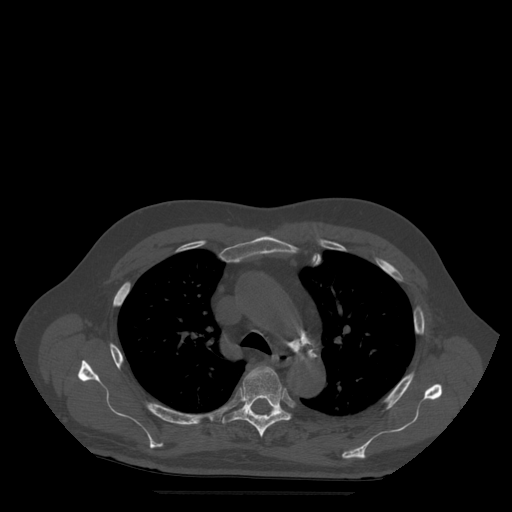
CT including the spine, one axial slice. Position 374 of 522 along the scan axis. Bone window (W 1800 / L 400 HU). 1.25 mm slice thickness. 512 × 512 image matrix, field of view 420 × 420 mm. Patient age 72 years. Case-level facts recorded for this patient, not image findings: primary cancer: prostate.
Structures marked on this image (semi-automatic segmentation, software-assisted and operator-edited):
- T5 vertebra: bounding box (x1, y1, x2, y2) in pixels: (223, 366, 291, 438)